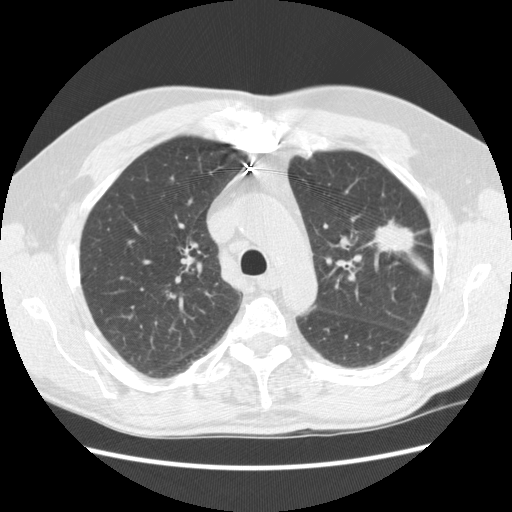
Low-dose screening chest CT, one axial slice; position 170 of 231 along the scan axis; lung window (W 1500 / L -600 HU); 512 × 512 image matrix, field of view 362 × 362 mm.
Structures marked on this image (manually delineated by an expert):
- lesion 1 (tumor, upper lobe of left lung): bounding box [x1, y1, x2, y2] px = [372, 220, 416, 254]